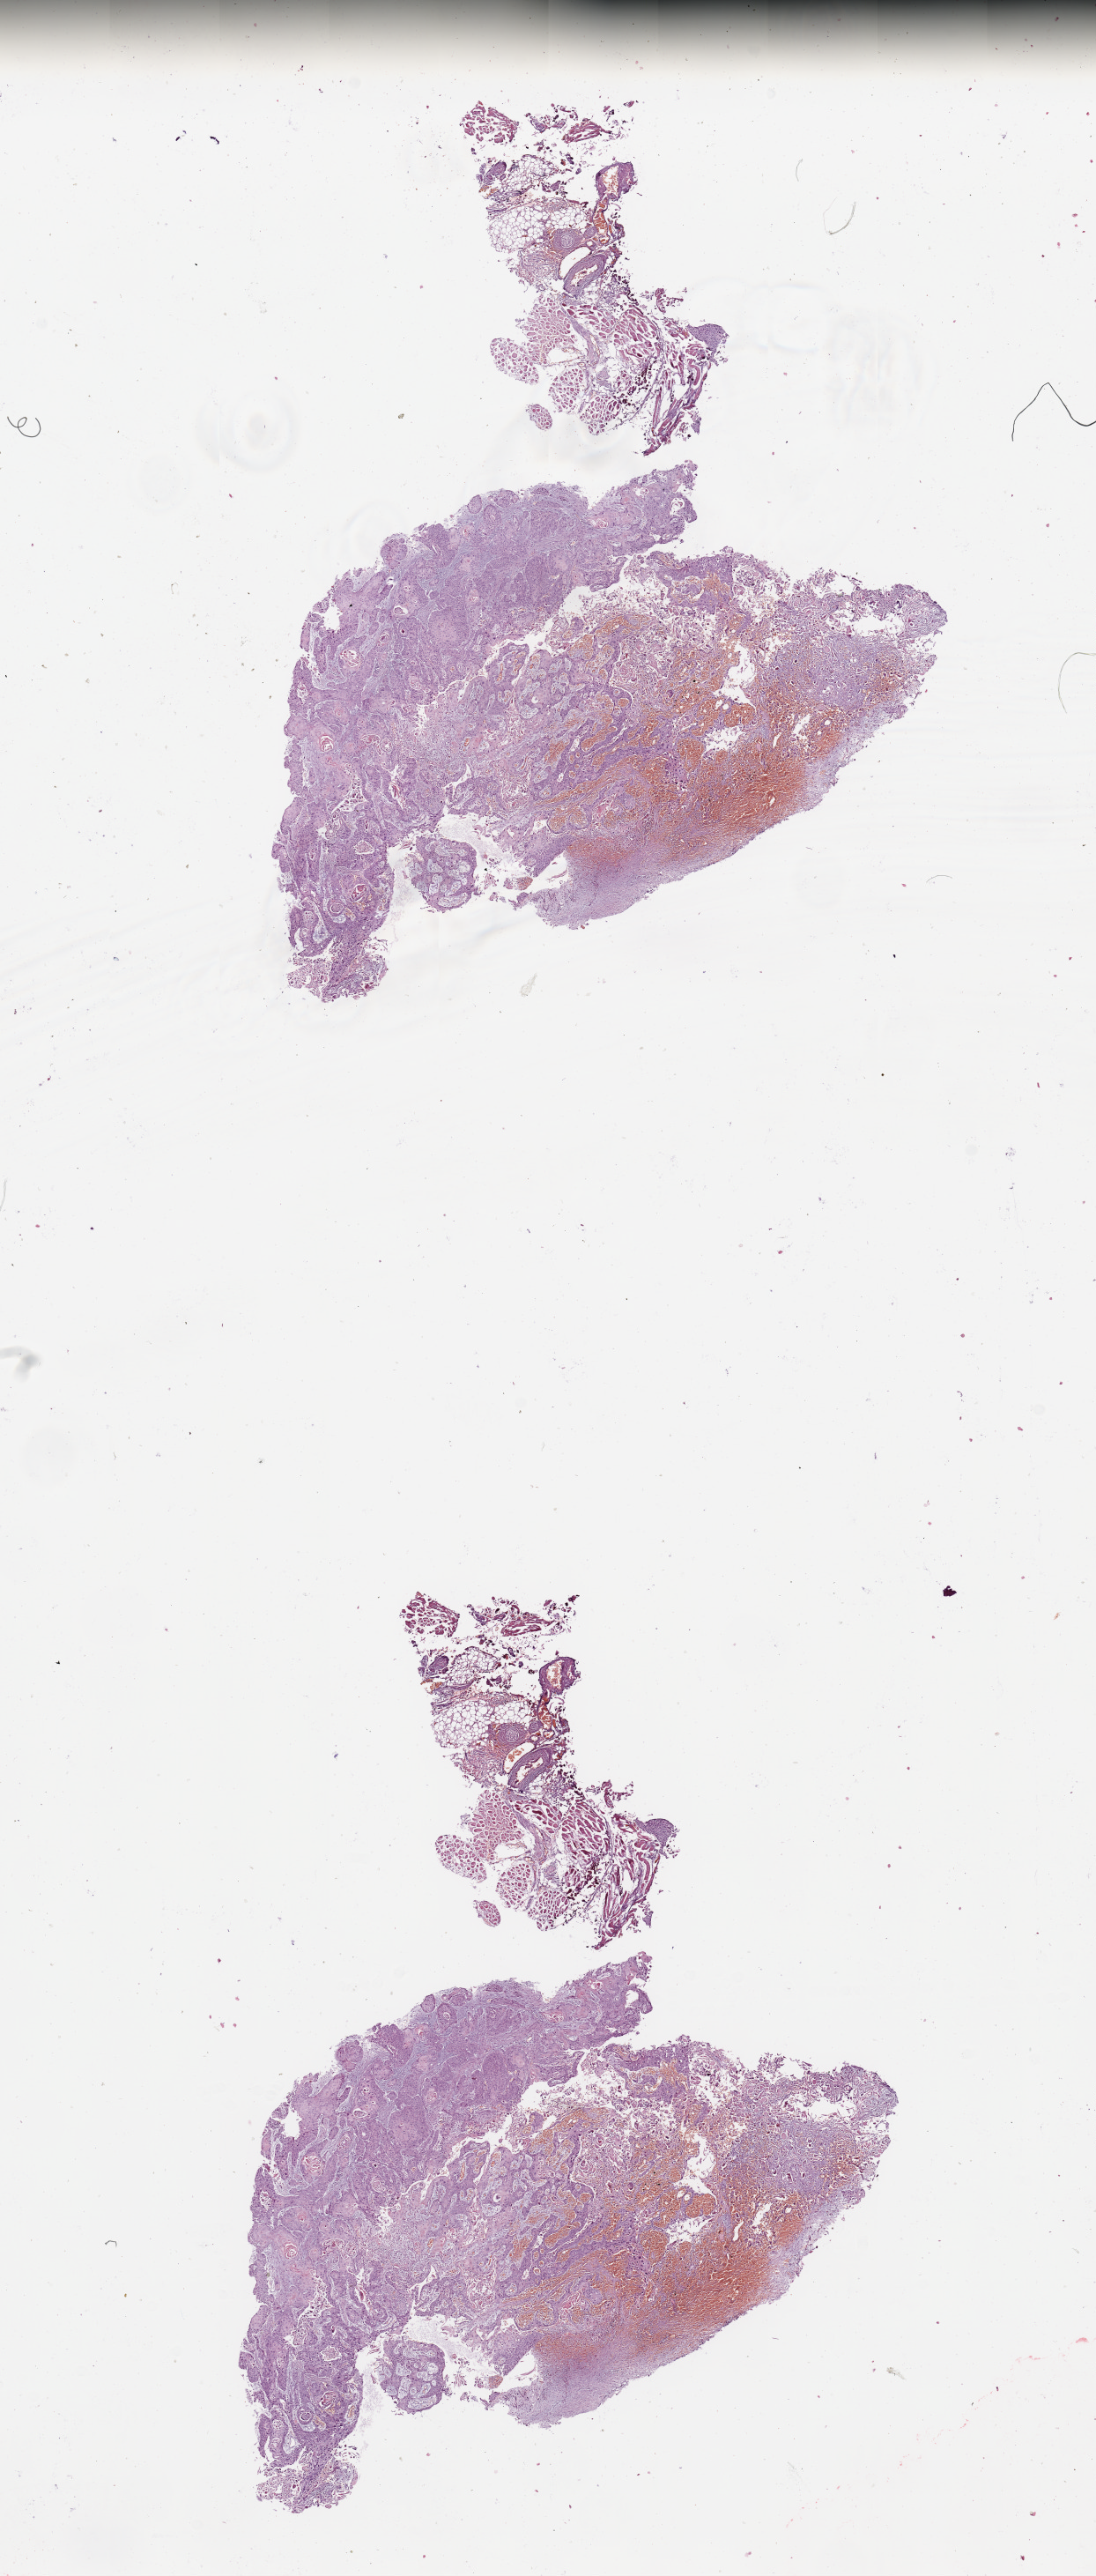
Whole-slide histology image, Hematoxylin and eosin (H&E) stained — whole scanned area (about 9.8 x 23.1 mm) shown as a low-resolution overview. Head and neck, tissue type not recorded. Male, 58 y/o.
Patient diagnosis: Squamous cell carcinoma, NOS (floor of mouth, NOS).